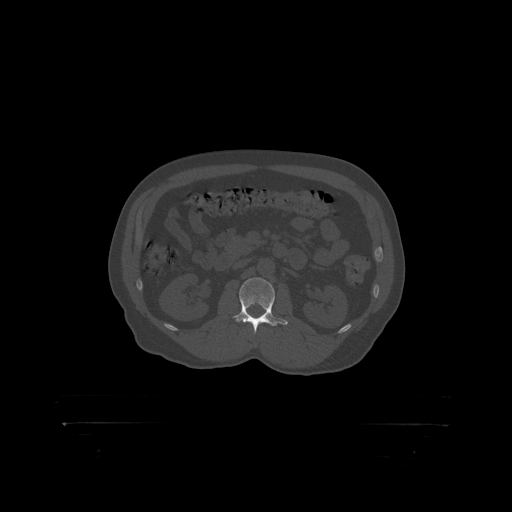
CT including the spine, one axial slice. Position 297 of 399 along the scan axis. Bone window (W 1800 / L 400 HU). 1.25 mm slice thickness. 512 × 512 image matrix. Male patient, age 46 years. From the clinical record (not read from this slice): primary cancer: skin.
Annotated regions visible in this slice (semi-automatic segmentation, software-assisted and operator-edited):
- L2 vertebra: box from (x=238, y=278) to (x=275, y=319) px